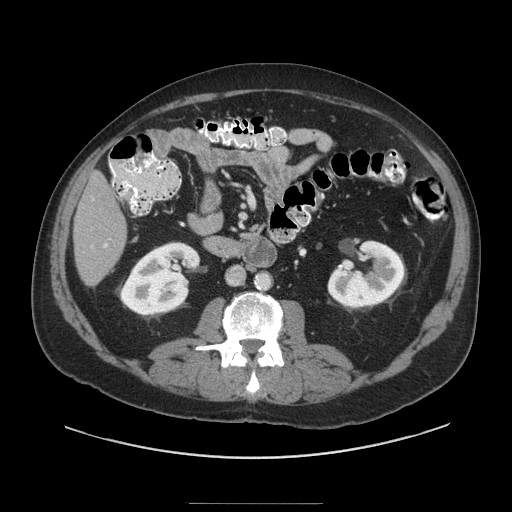
Contrast-enhanced abdominal CT (liver protocol), one axial slice; slice 26 of 91 in the series (ordered by position); 140 kVp; soft-tissue window (W 400 / L 40 HU); 512 × 512 image matrix, field of view 440 × 440 mm. Case-level facts recorded for this patient, not image findings: diagnosis: hepatocellular carcinoma (patient treated with transarterial chemoembolisation; whether this scan precedes or follows treatment is not stated here); TNM stage (as recorded): Stage-I; Child-Pugh class: A; tumour nodularity: uninodular.
Outlined on this slice (semi-automatically segmented with operator editing):
- liver parenchyma outside the tumour (the mass and vessels are separate outlines, so this box may not span the whole liver): bounding box [x1, y1, x2, y2] px = [74, 172, 126, 286]
- liver vessels: [103, 244, 108, 248]